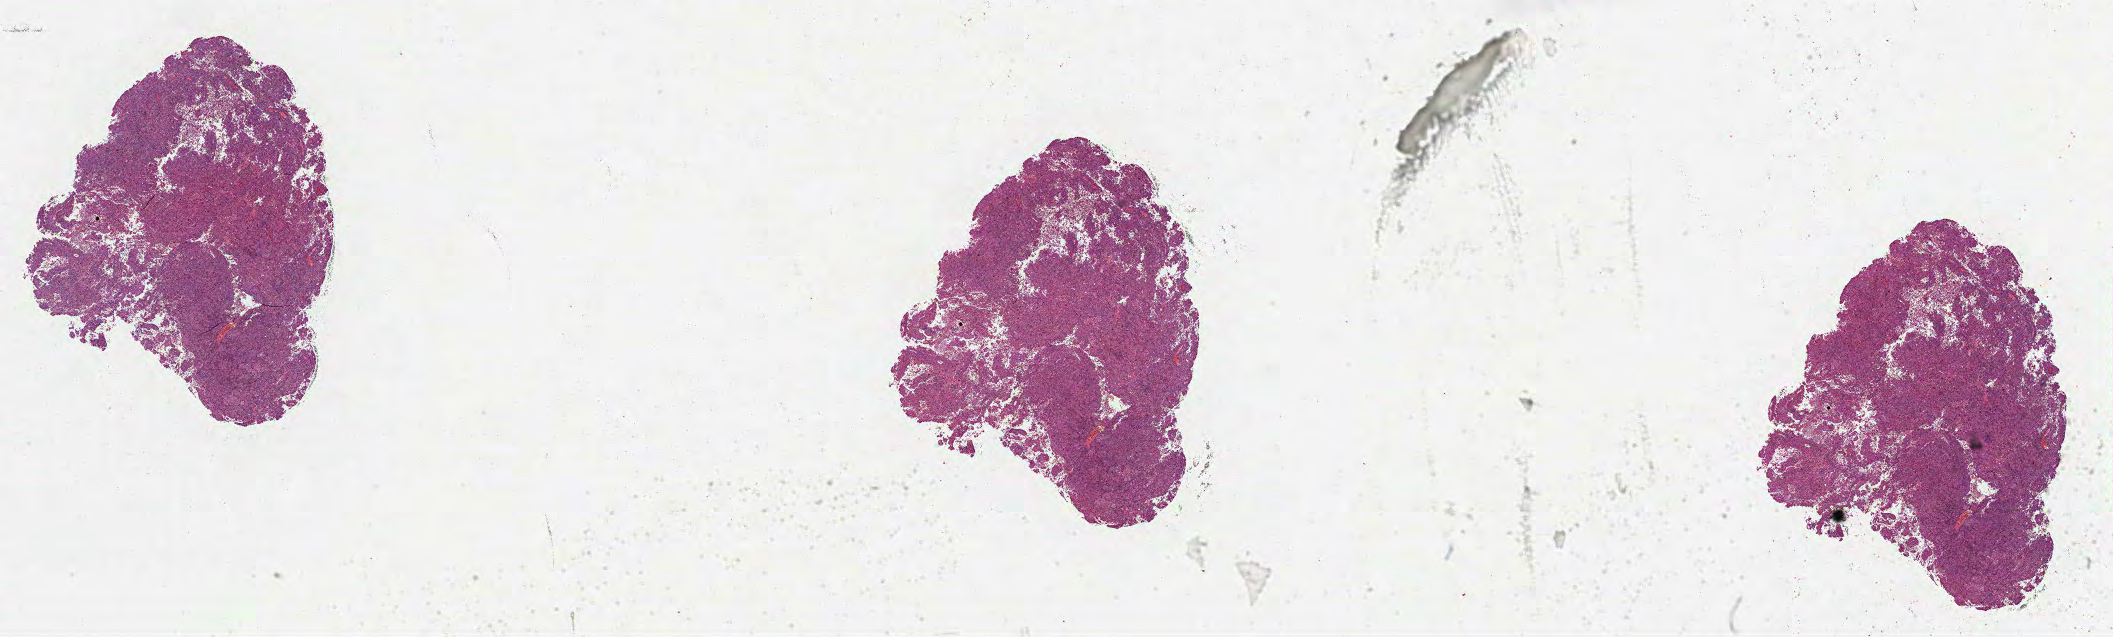
Hematoxylin and eosin (H&E) stained whole-slide image — shown as a low-resolution overview of the whole scanned area (about 34.1 x 10.3 mm, acquisition: 40x scan). Formalin-fixed paraffin-embedded (FFPE) diagnostic section. Primary tumour sample from the lung. Female patient; age at initial diagnosis 47 years.
AJCC pathologic stage: IIIA. Laterality: right. Diagnosis: Squamous cell carcinoma, NOS. TNM: T3 N1 M0.